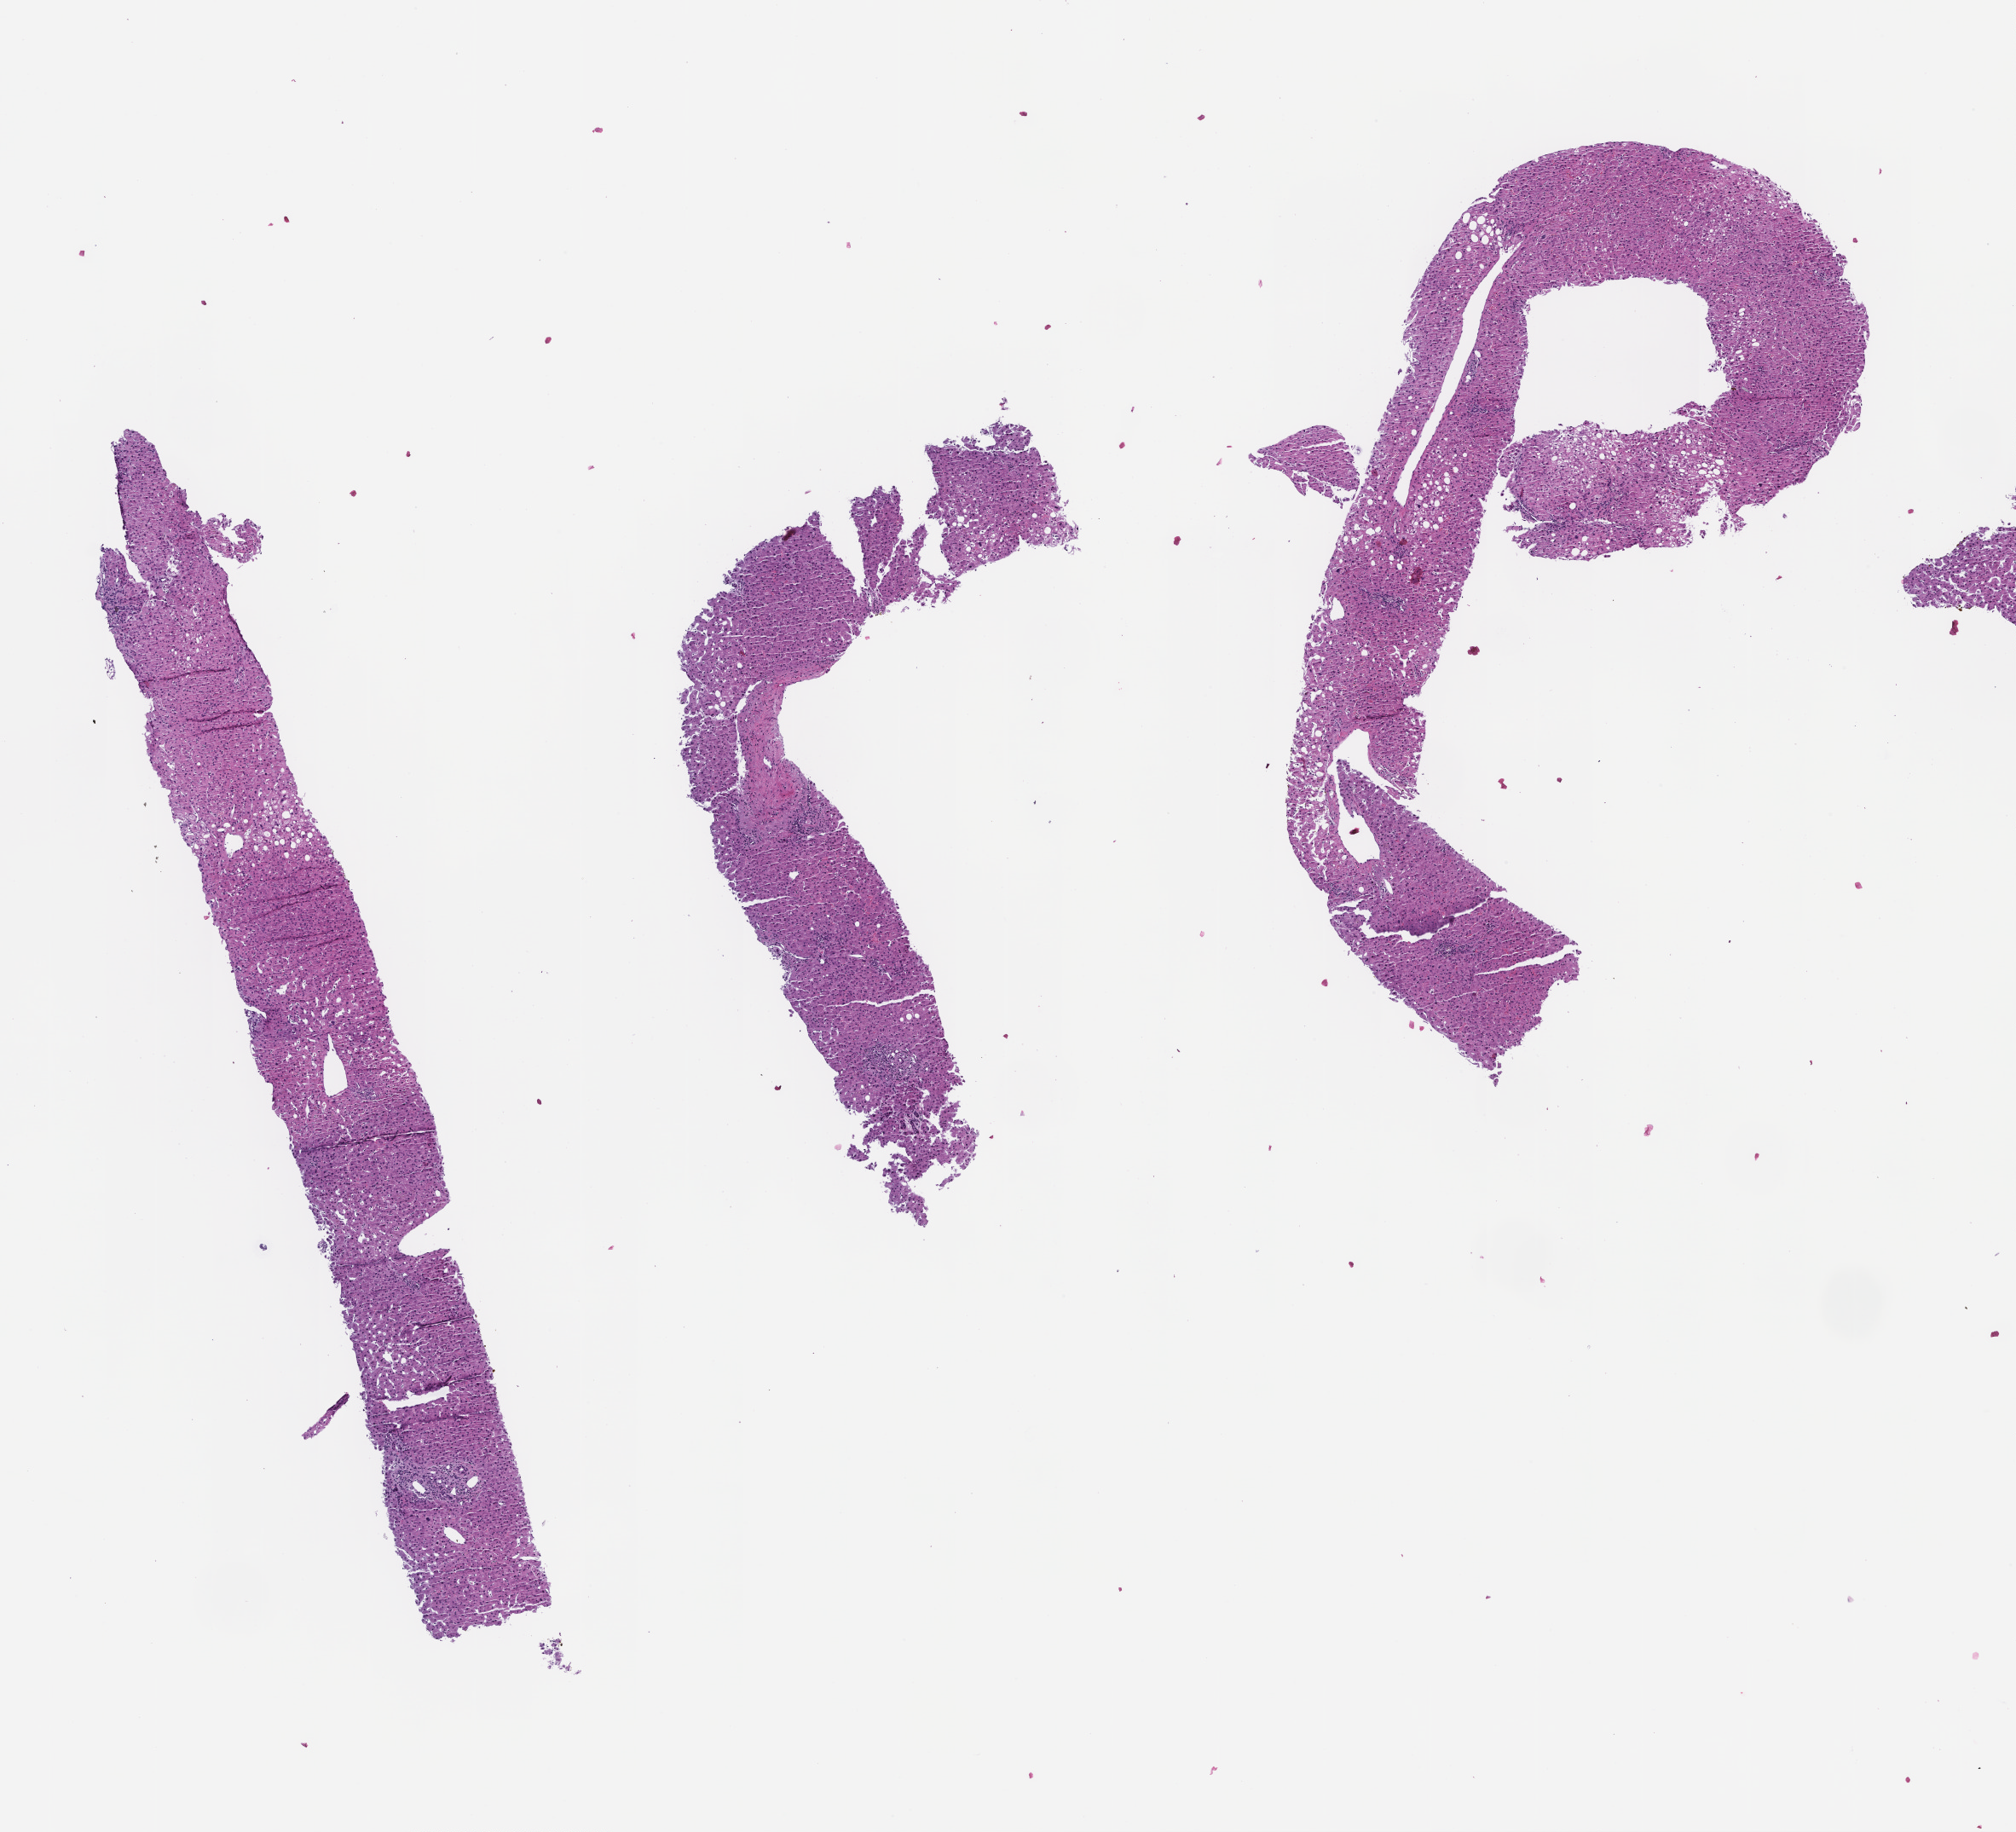
Digitized H&E-stained section, a low-resolution overview of the entire scanned area, about 9.5 x 8.7 mm. FFPE section. Collected at baseline (before treatment). Male patient.
This section: metastasis (sampled organ not recorded). Patient diagnosis (primary): Colorectal Carcinoma.